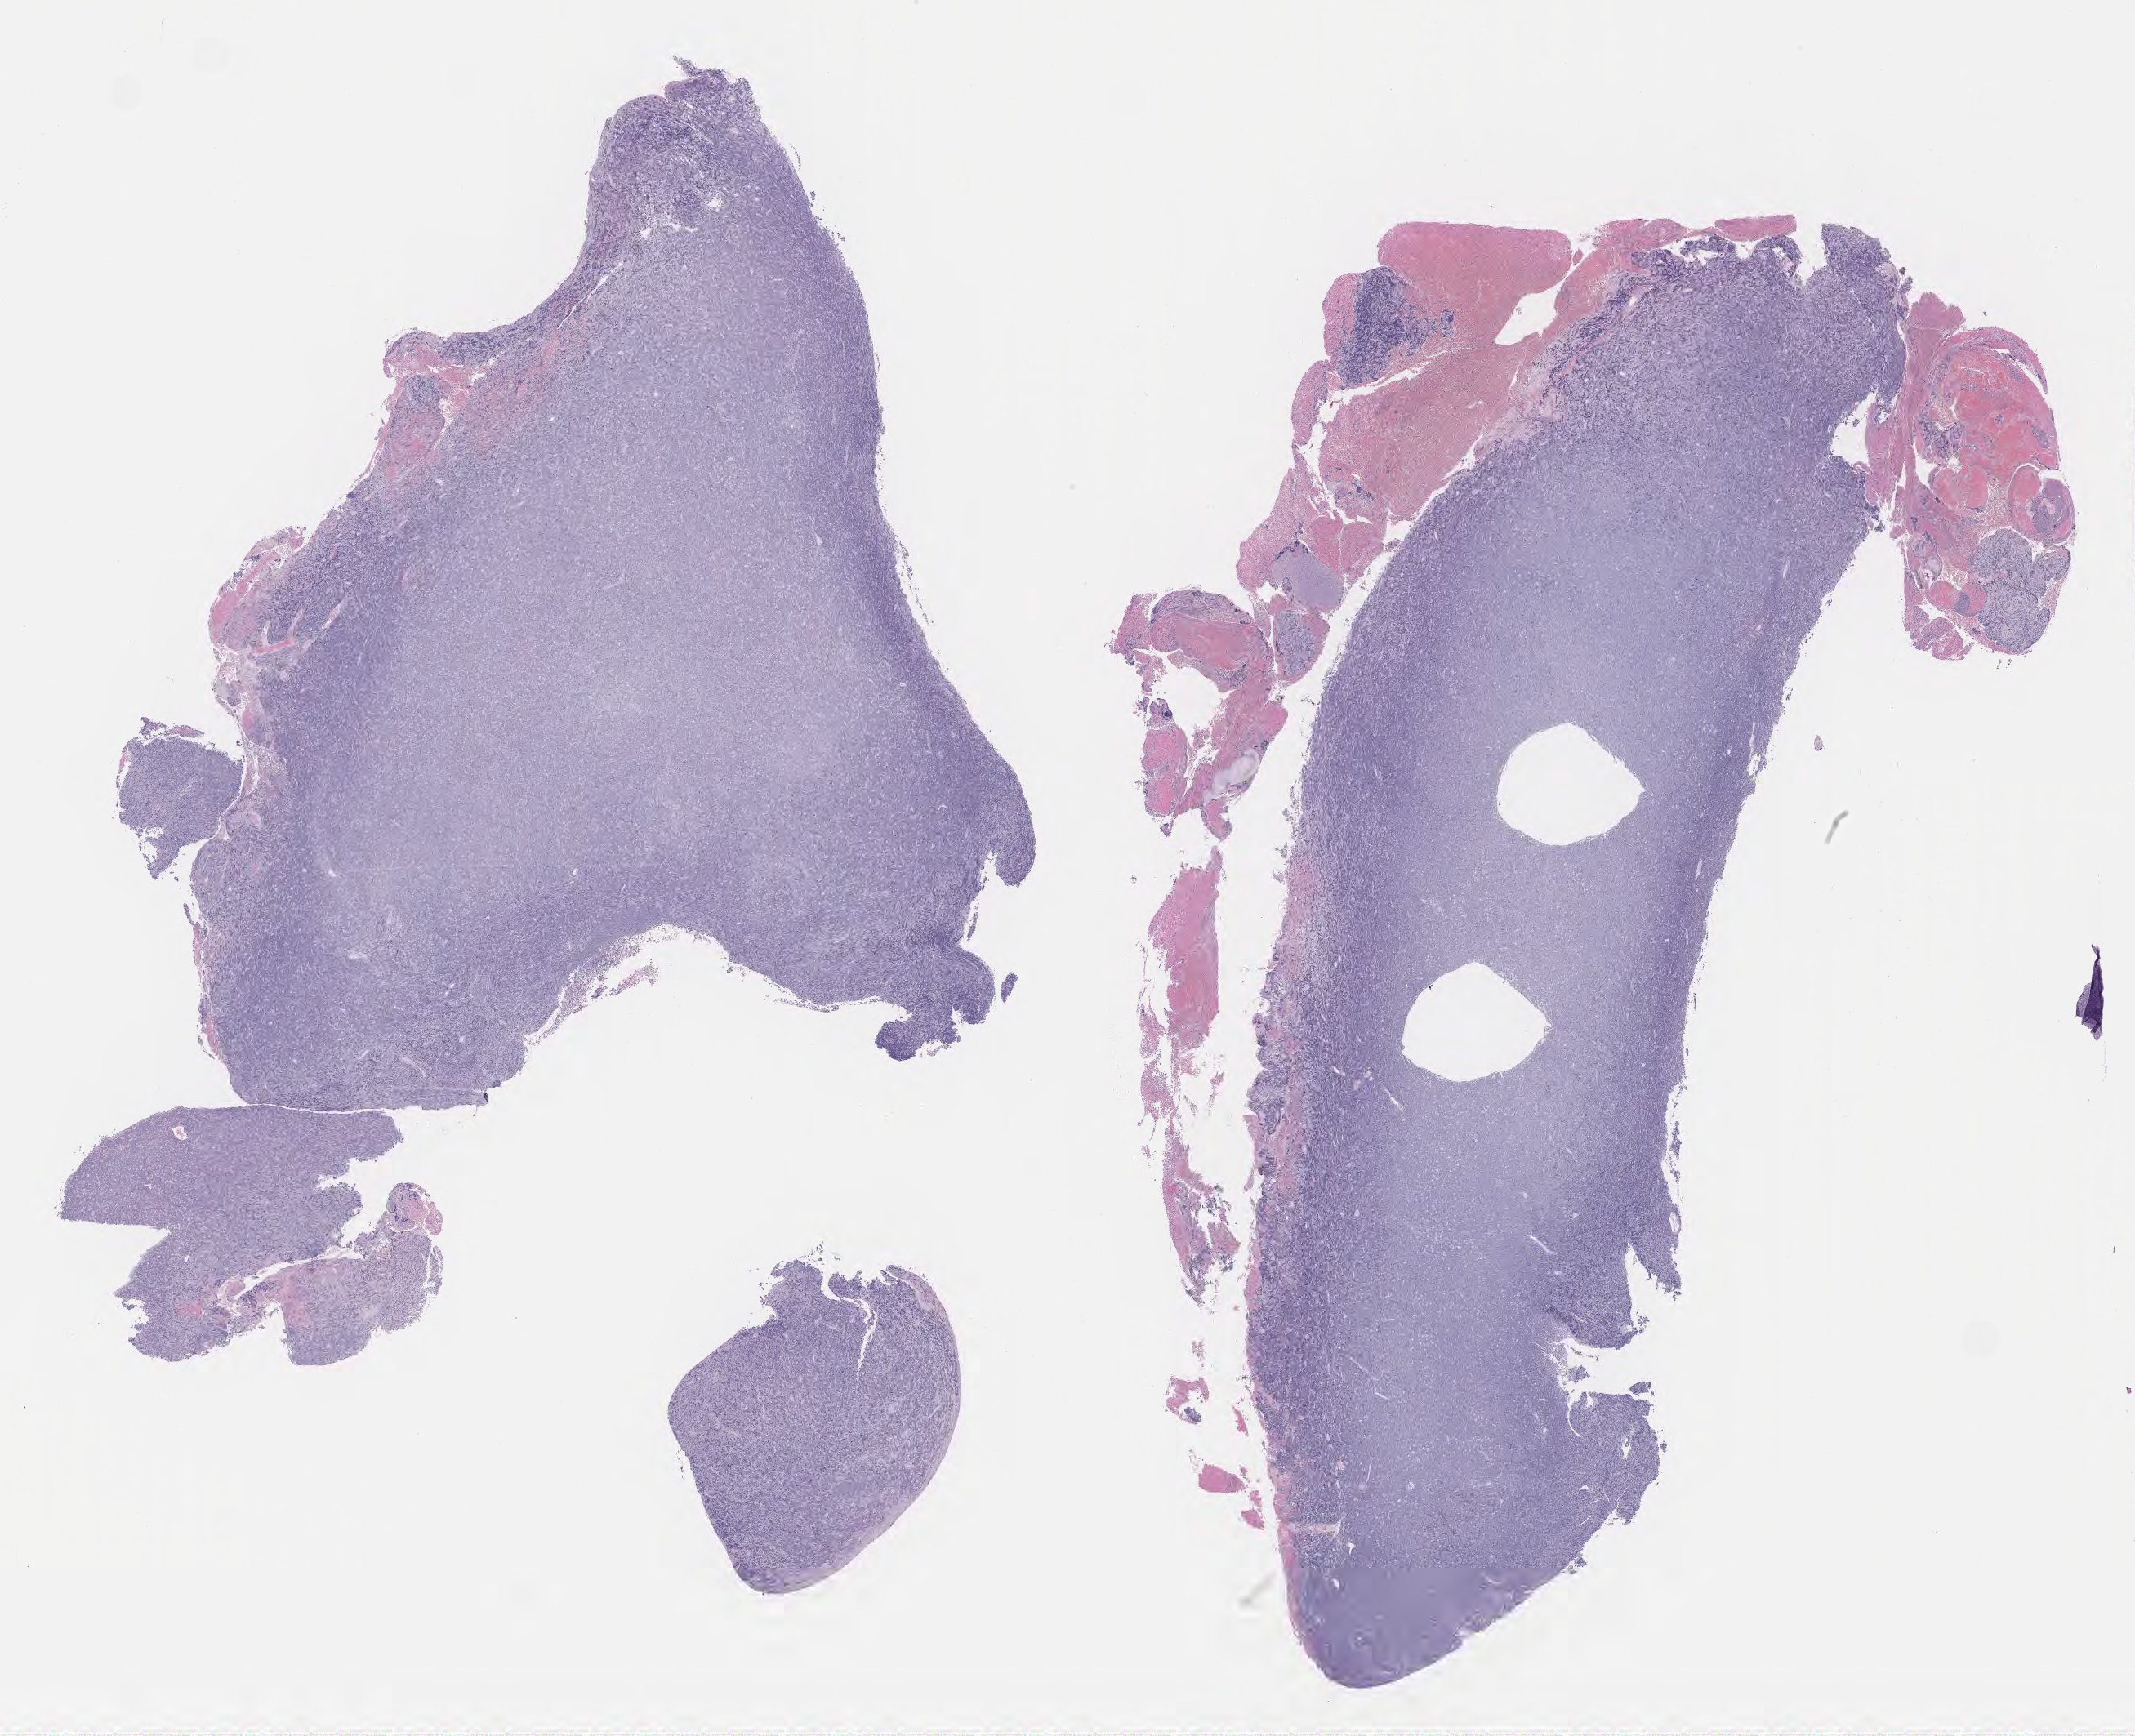
Digitized H&E-stained section — a low-resolution overview of the entire scanned area, about 21.1 x 17.2 mm. Specimen: tumor tissue. Site: female genitalia. Patient female; aged 61.
* histologic diagnosis: Burkitt lymphoma, NOS